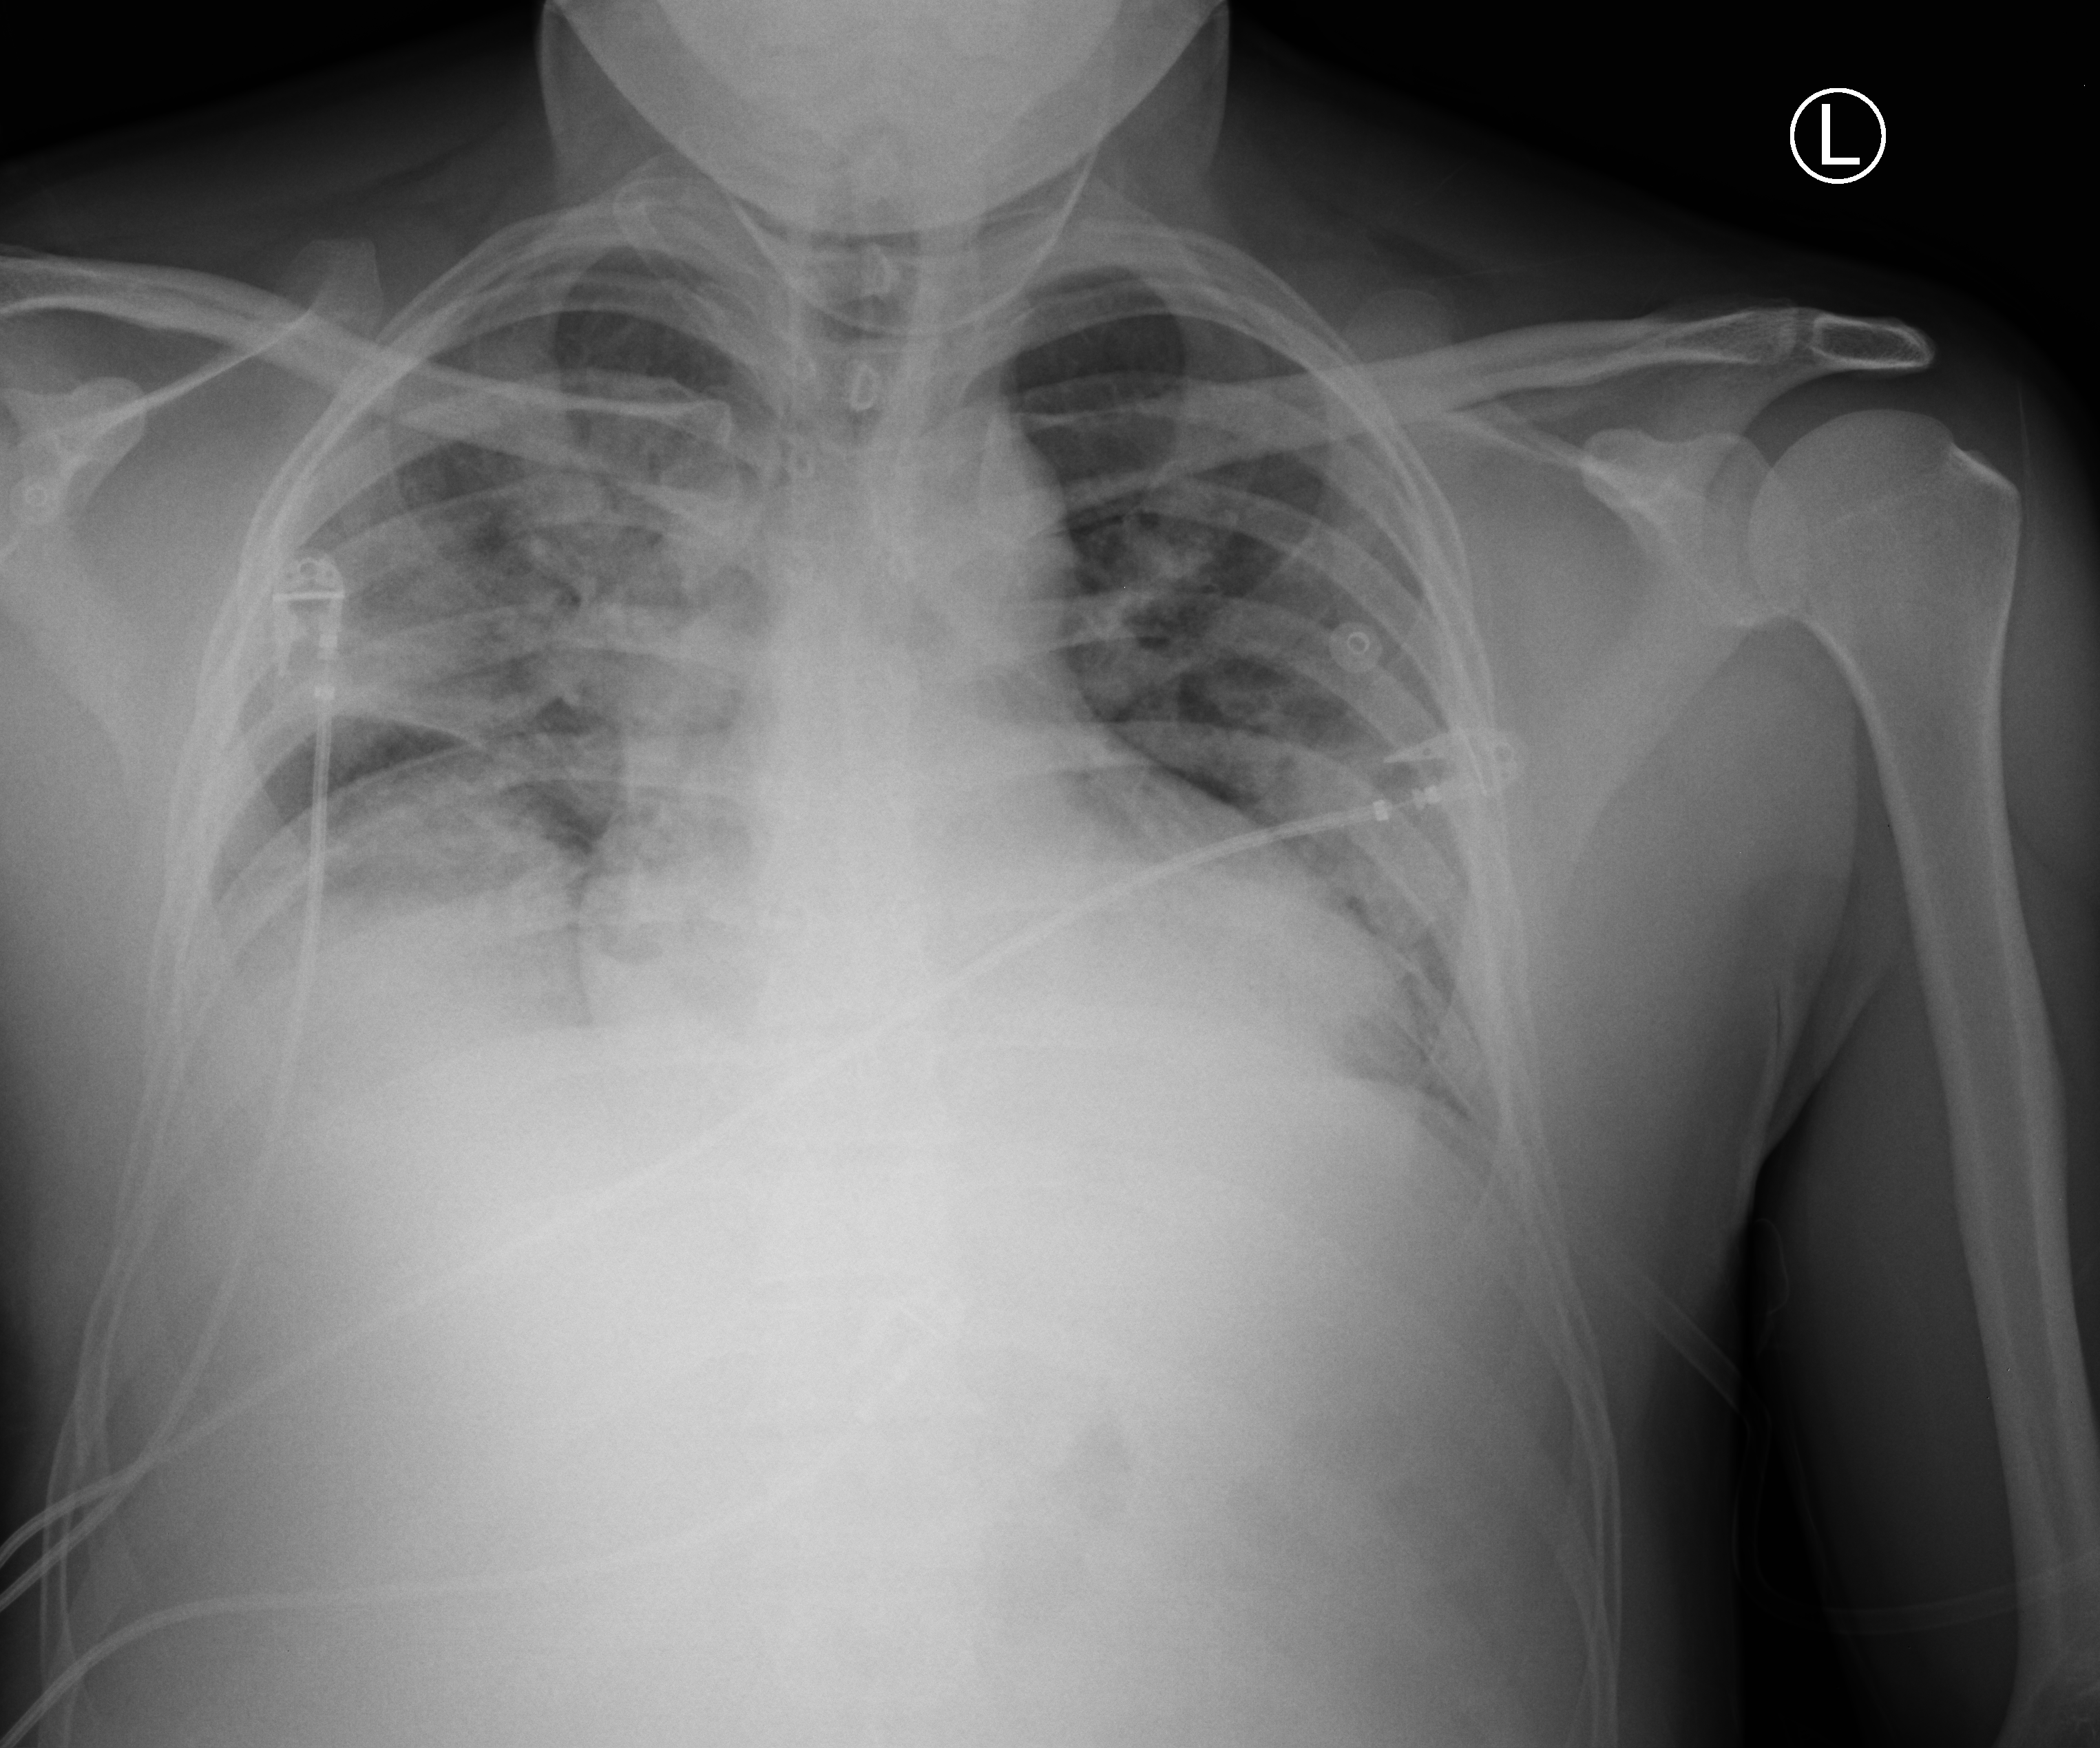
Bedside chest radiograph (computed radiography); anteroposterior (AP) projection. Male patient hospitalised with COVID-19, age 18–59 years.
Admission-level facts for this patient (not findings on this image; timing relative to this image not recorded):
- COPD (admission record): no
- length of hospital stay: 15 days
- other chronic lung disease (admission record): no